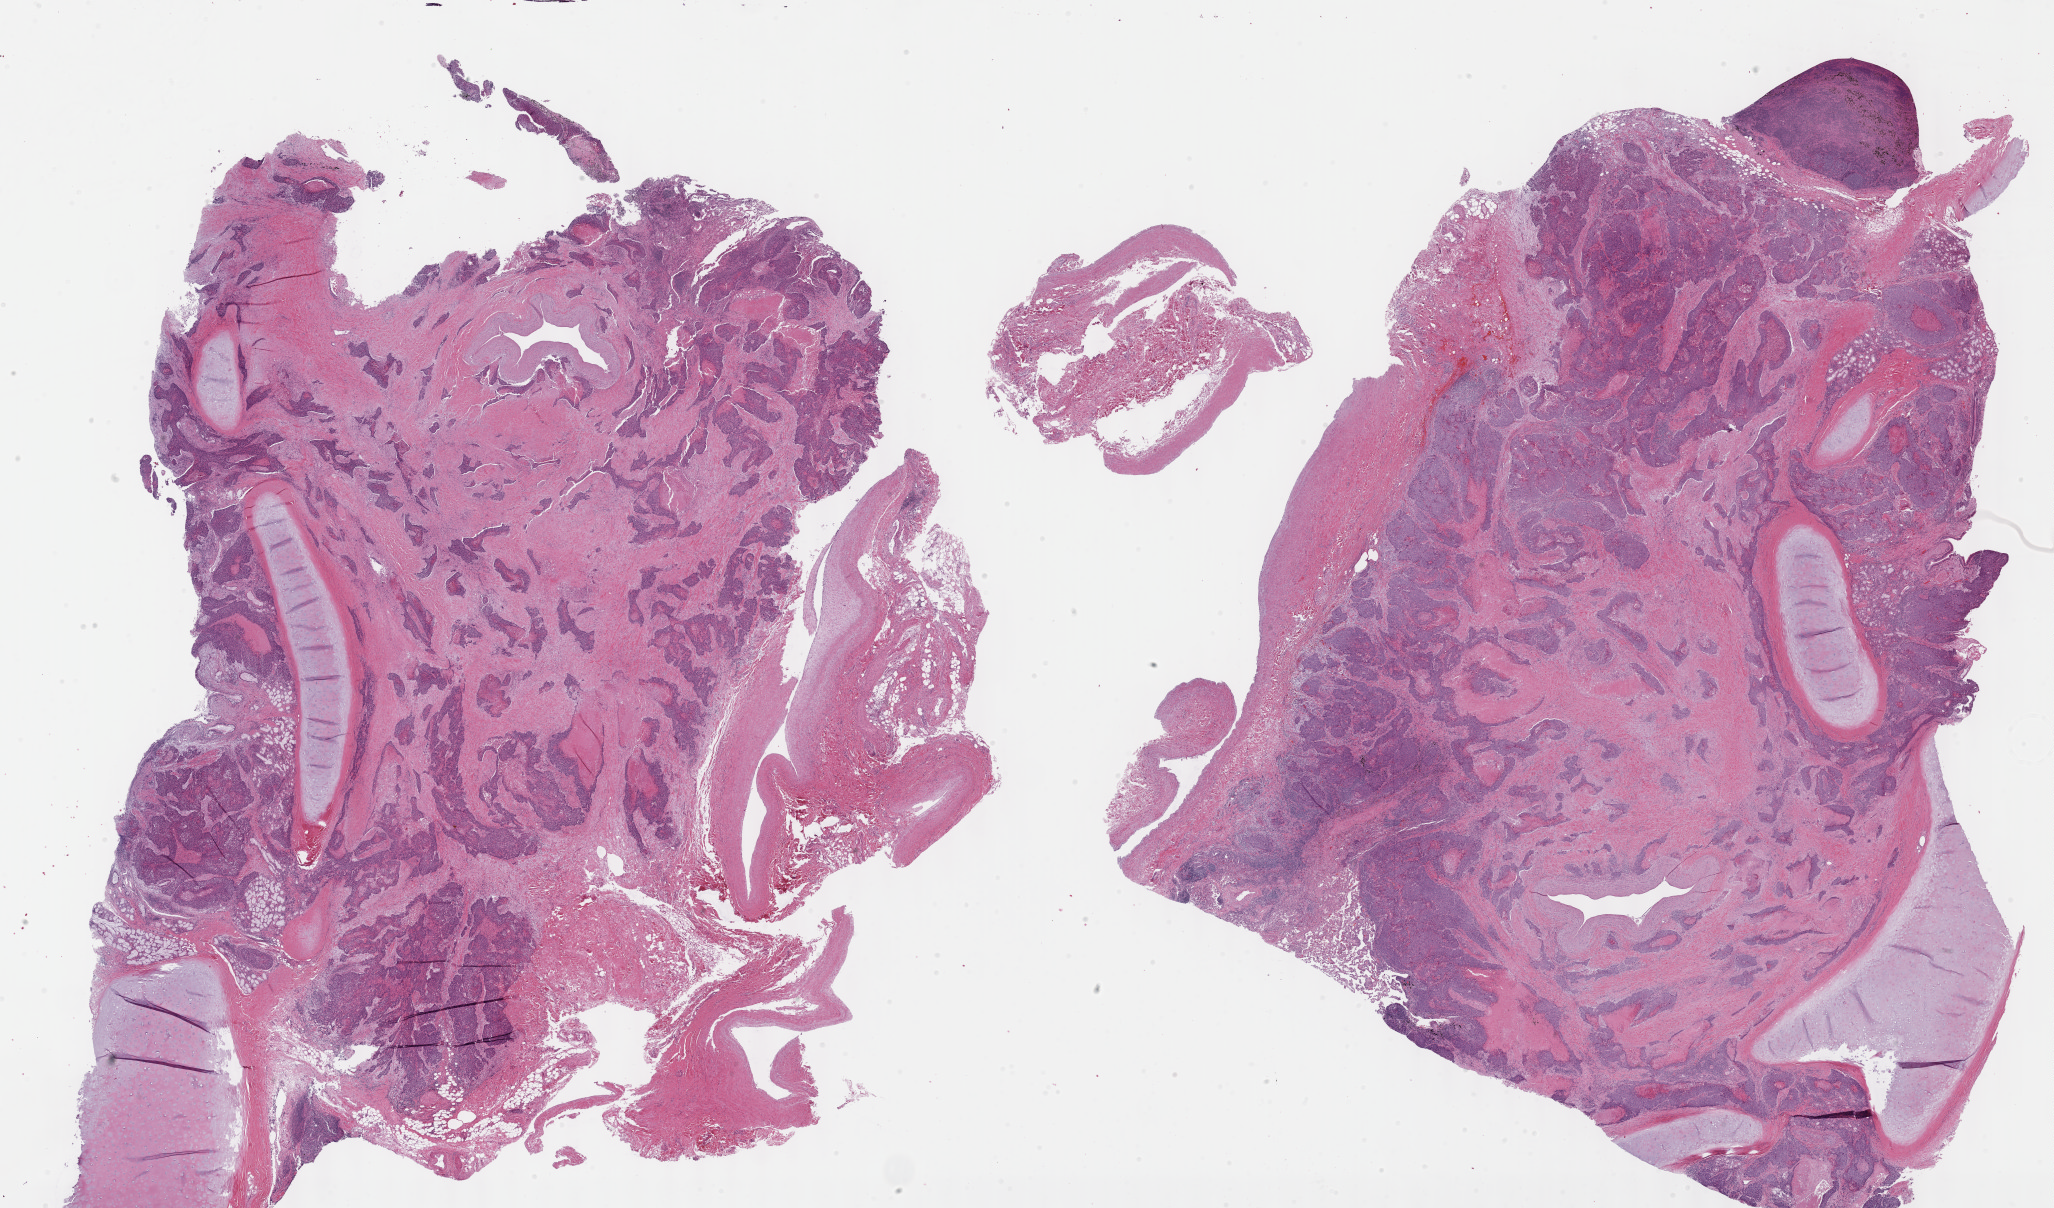
Hematoxylin and eosin (H&E) stained whole-slide image, shown as a low-resolution overview of the whole scanned area (about 33.2 x 19.5 mm). Formalin-fixed paraffin-embedded (FFPE) diagnostic section. Lung, primary tumour sample. Patient: male, age at initial diagnosis 73 years.
Pathologic diagnosis: Squamous cell carcinoma, NOS (upper lobe, lung).